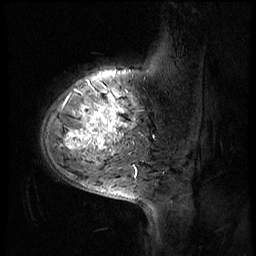
Breast MRI (dynamic contrast-enhanced), one sagittal slice; position 12 of 56 along the scan axis; 4 images stored at this slice position (order not interpretable as contrast timing); 1.5 T; TE 4.2 ms, TR 8.9 ms; 2.5 mm slice thickness; 256 × 256 image matrix, field of view 220 × 220 mm. Female patient, age 51 years. From the clinical record (not read from this slice): setting: breast cancer imaged before/during neoadjuvant chemotherapy; receptor status: triple-negative.
Annotated regions visible in this slice (semi-automatic segmentation, software-assisted and operator-edited):
- analysis volume of interest (the breast-tissue region the enhancement analysis was run in; not a lesion): bounding box (x1, y1, x2, y2) in pixels: (41, 70, 150, 173)
- tumour enhancement mask (voxels above the 140 % enhancement threshold inside the analysis volume of interest): (63, 102, 128, 149)